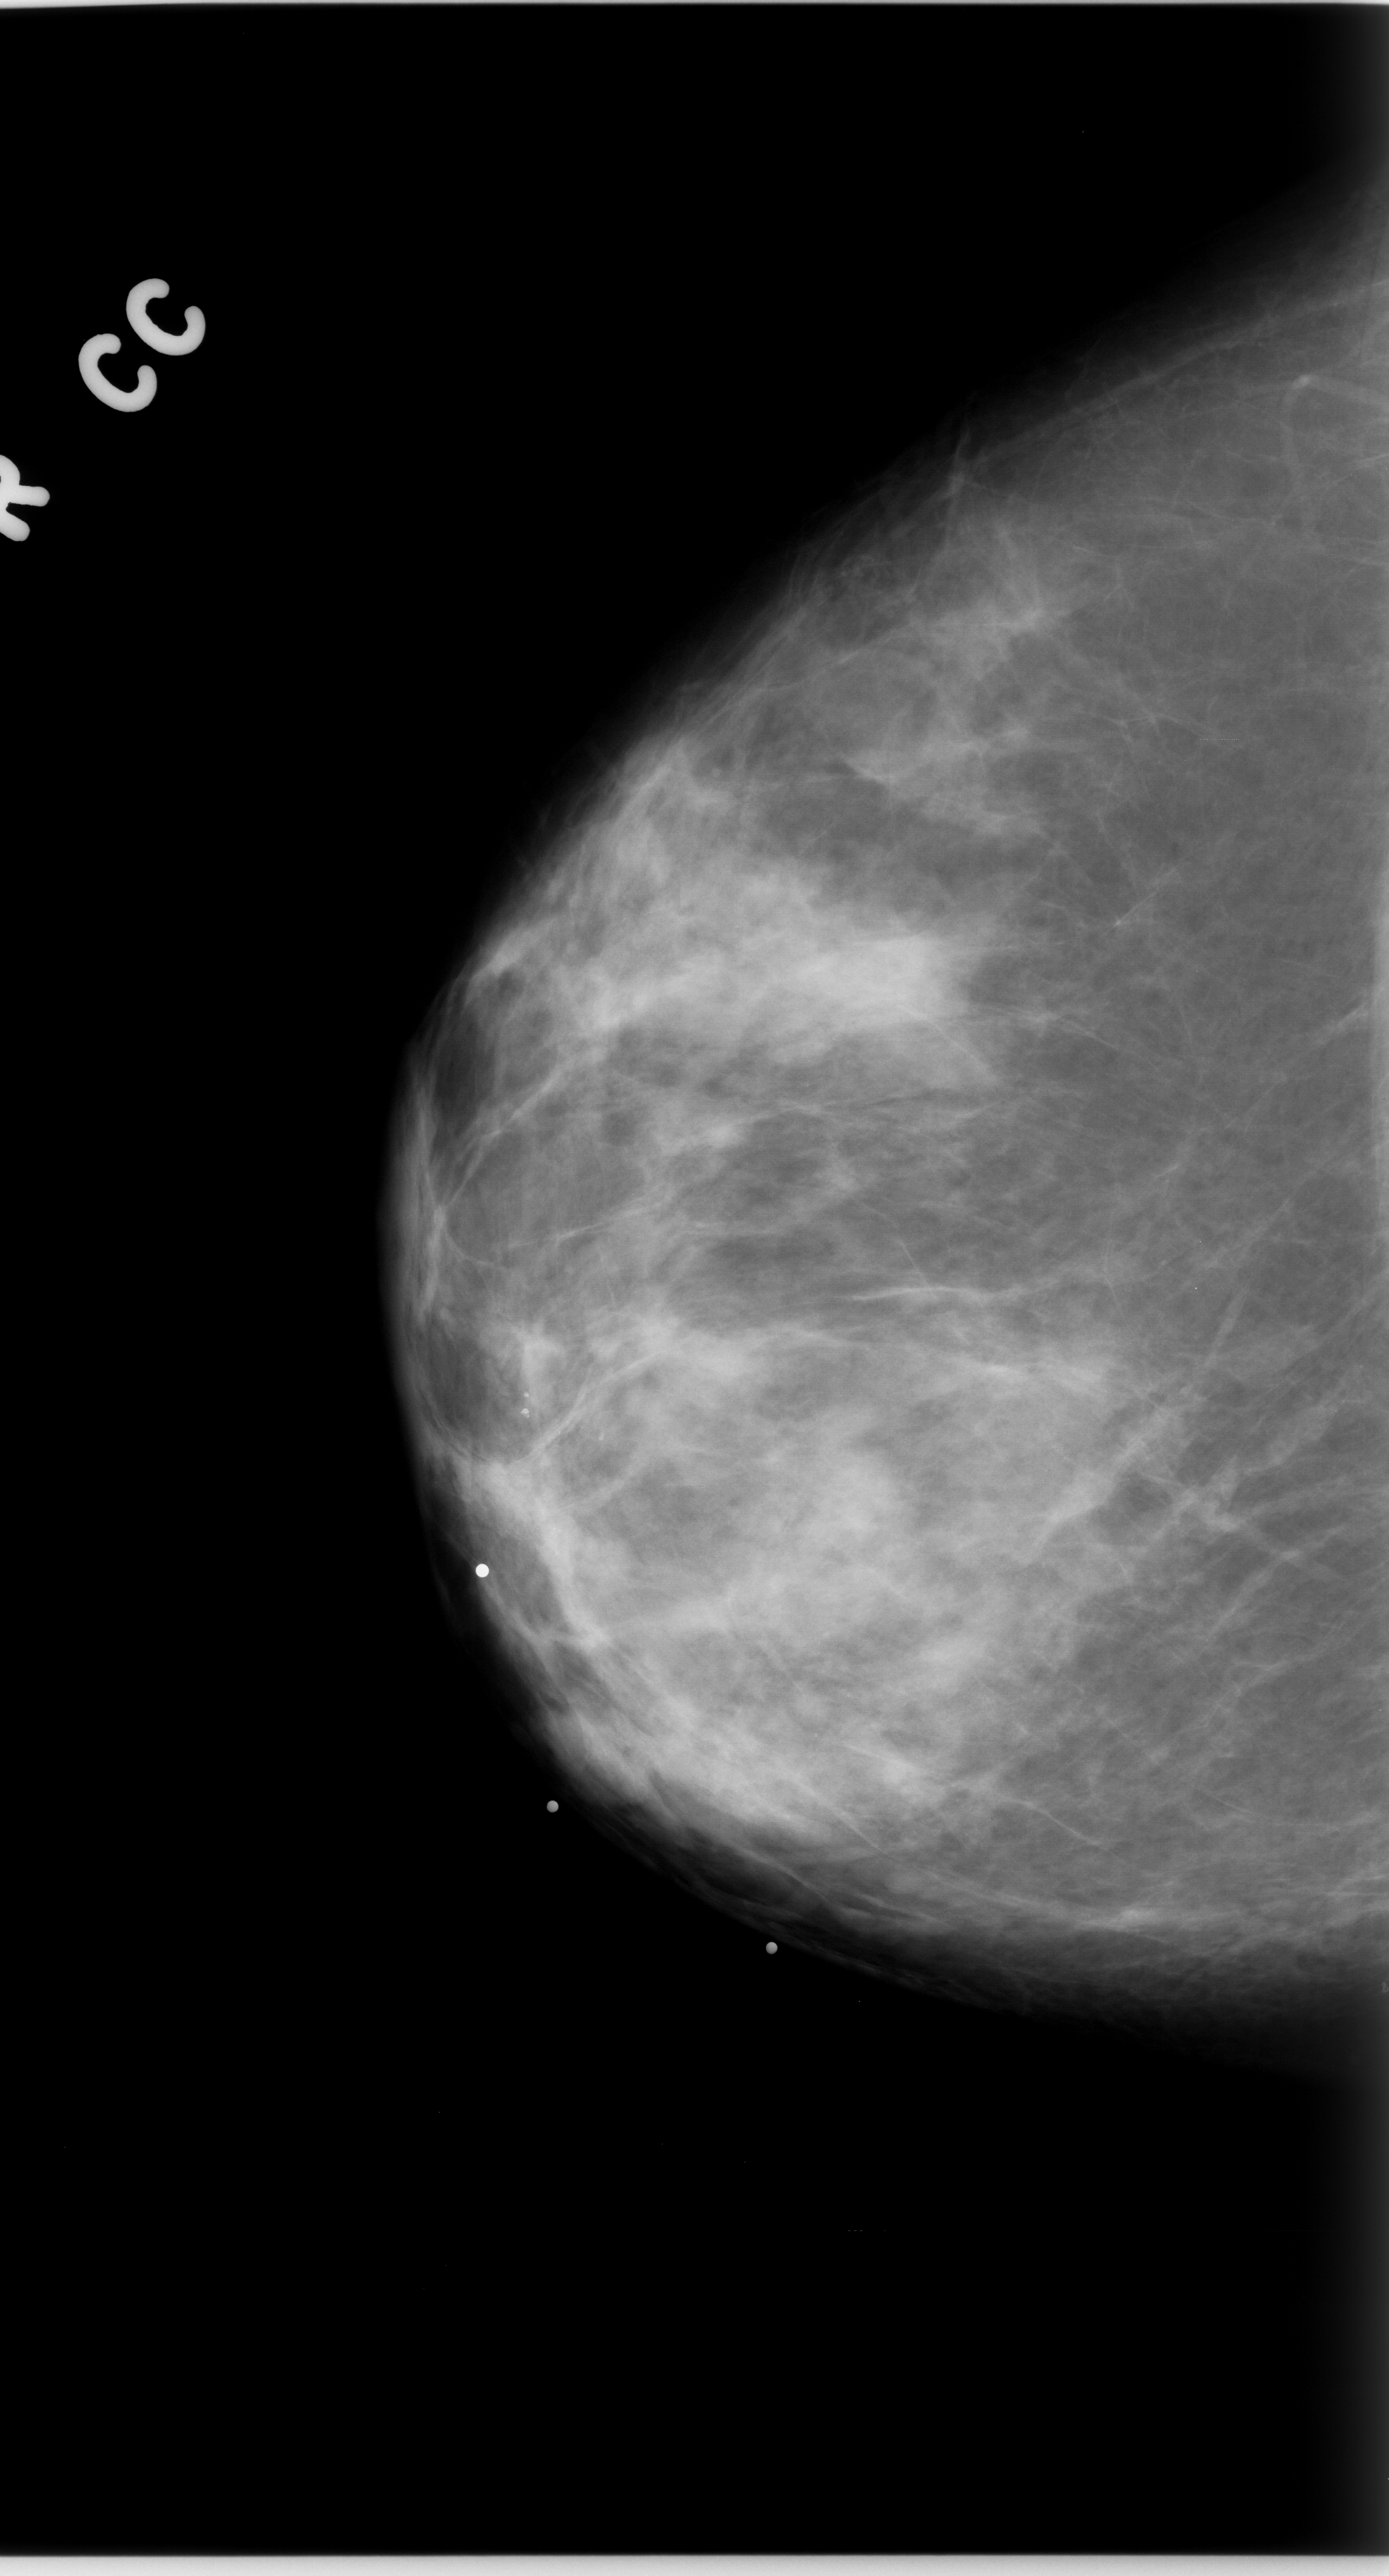
Mammogram (digitized film). Right breast. Craniocaudal (CC) view. BI-RADS breast density category 2 (scale 1–4). 1389 × 2576 image matrix.
Expert-marked regions of interest on this image (one box per marked abnormality):
- mass, shape oval, margins obscured; BI-RADS assessment category 4; pathology result (as recorded, not read from the image): malignant: box from (x=556, y=1681) to (x=680, y=1805) px